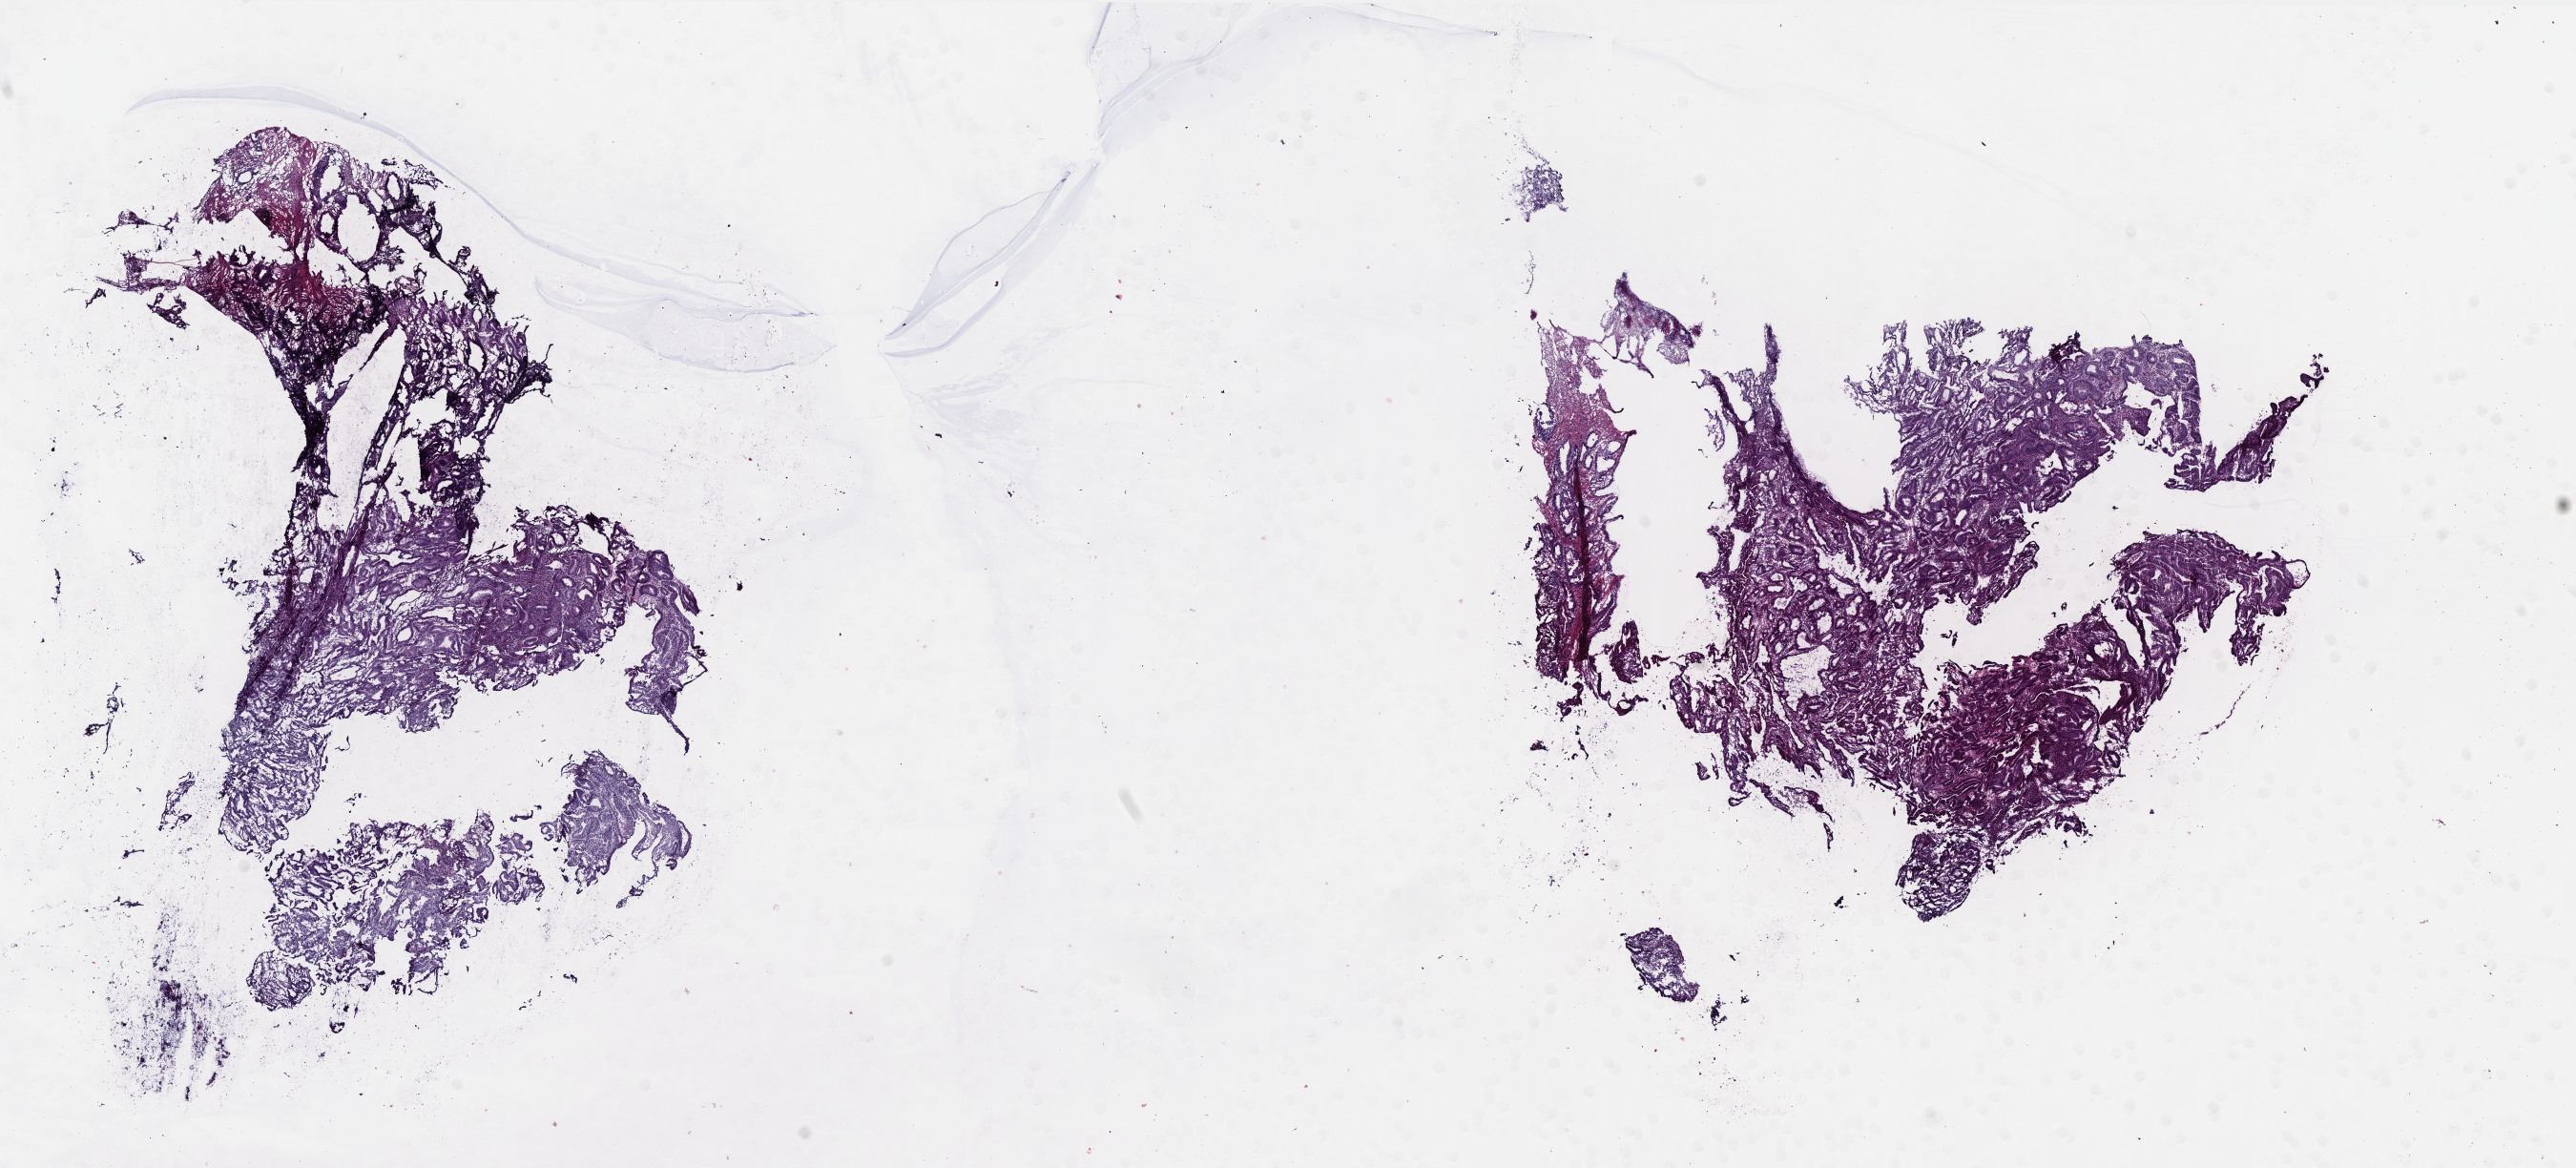
Digitized H&E-stained tissue section (whole slide) — a low-resolution overview of the entire scanned area, about 21.6 x 9.8 mm. Frozen section from the bottom of the tissue portion. Primary tumour sample from the uterus. Female patient; age at initial diagnosis 61 years. Composition of this section per pathologist review: tumour cells 0%, tumour nuclei 0%.
Diagnosis: Serous cystadenocarcinoma, NOS (endometrium).